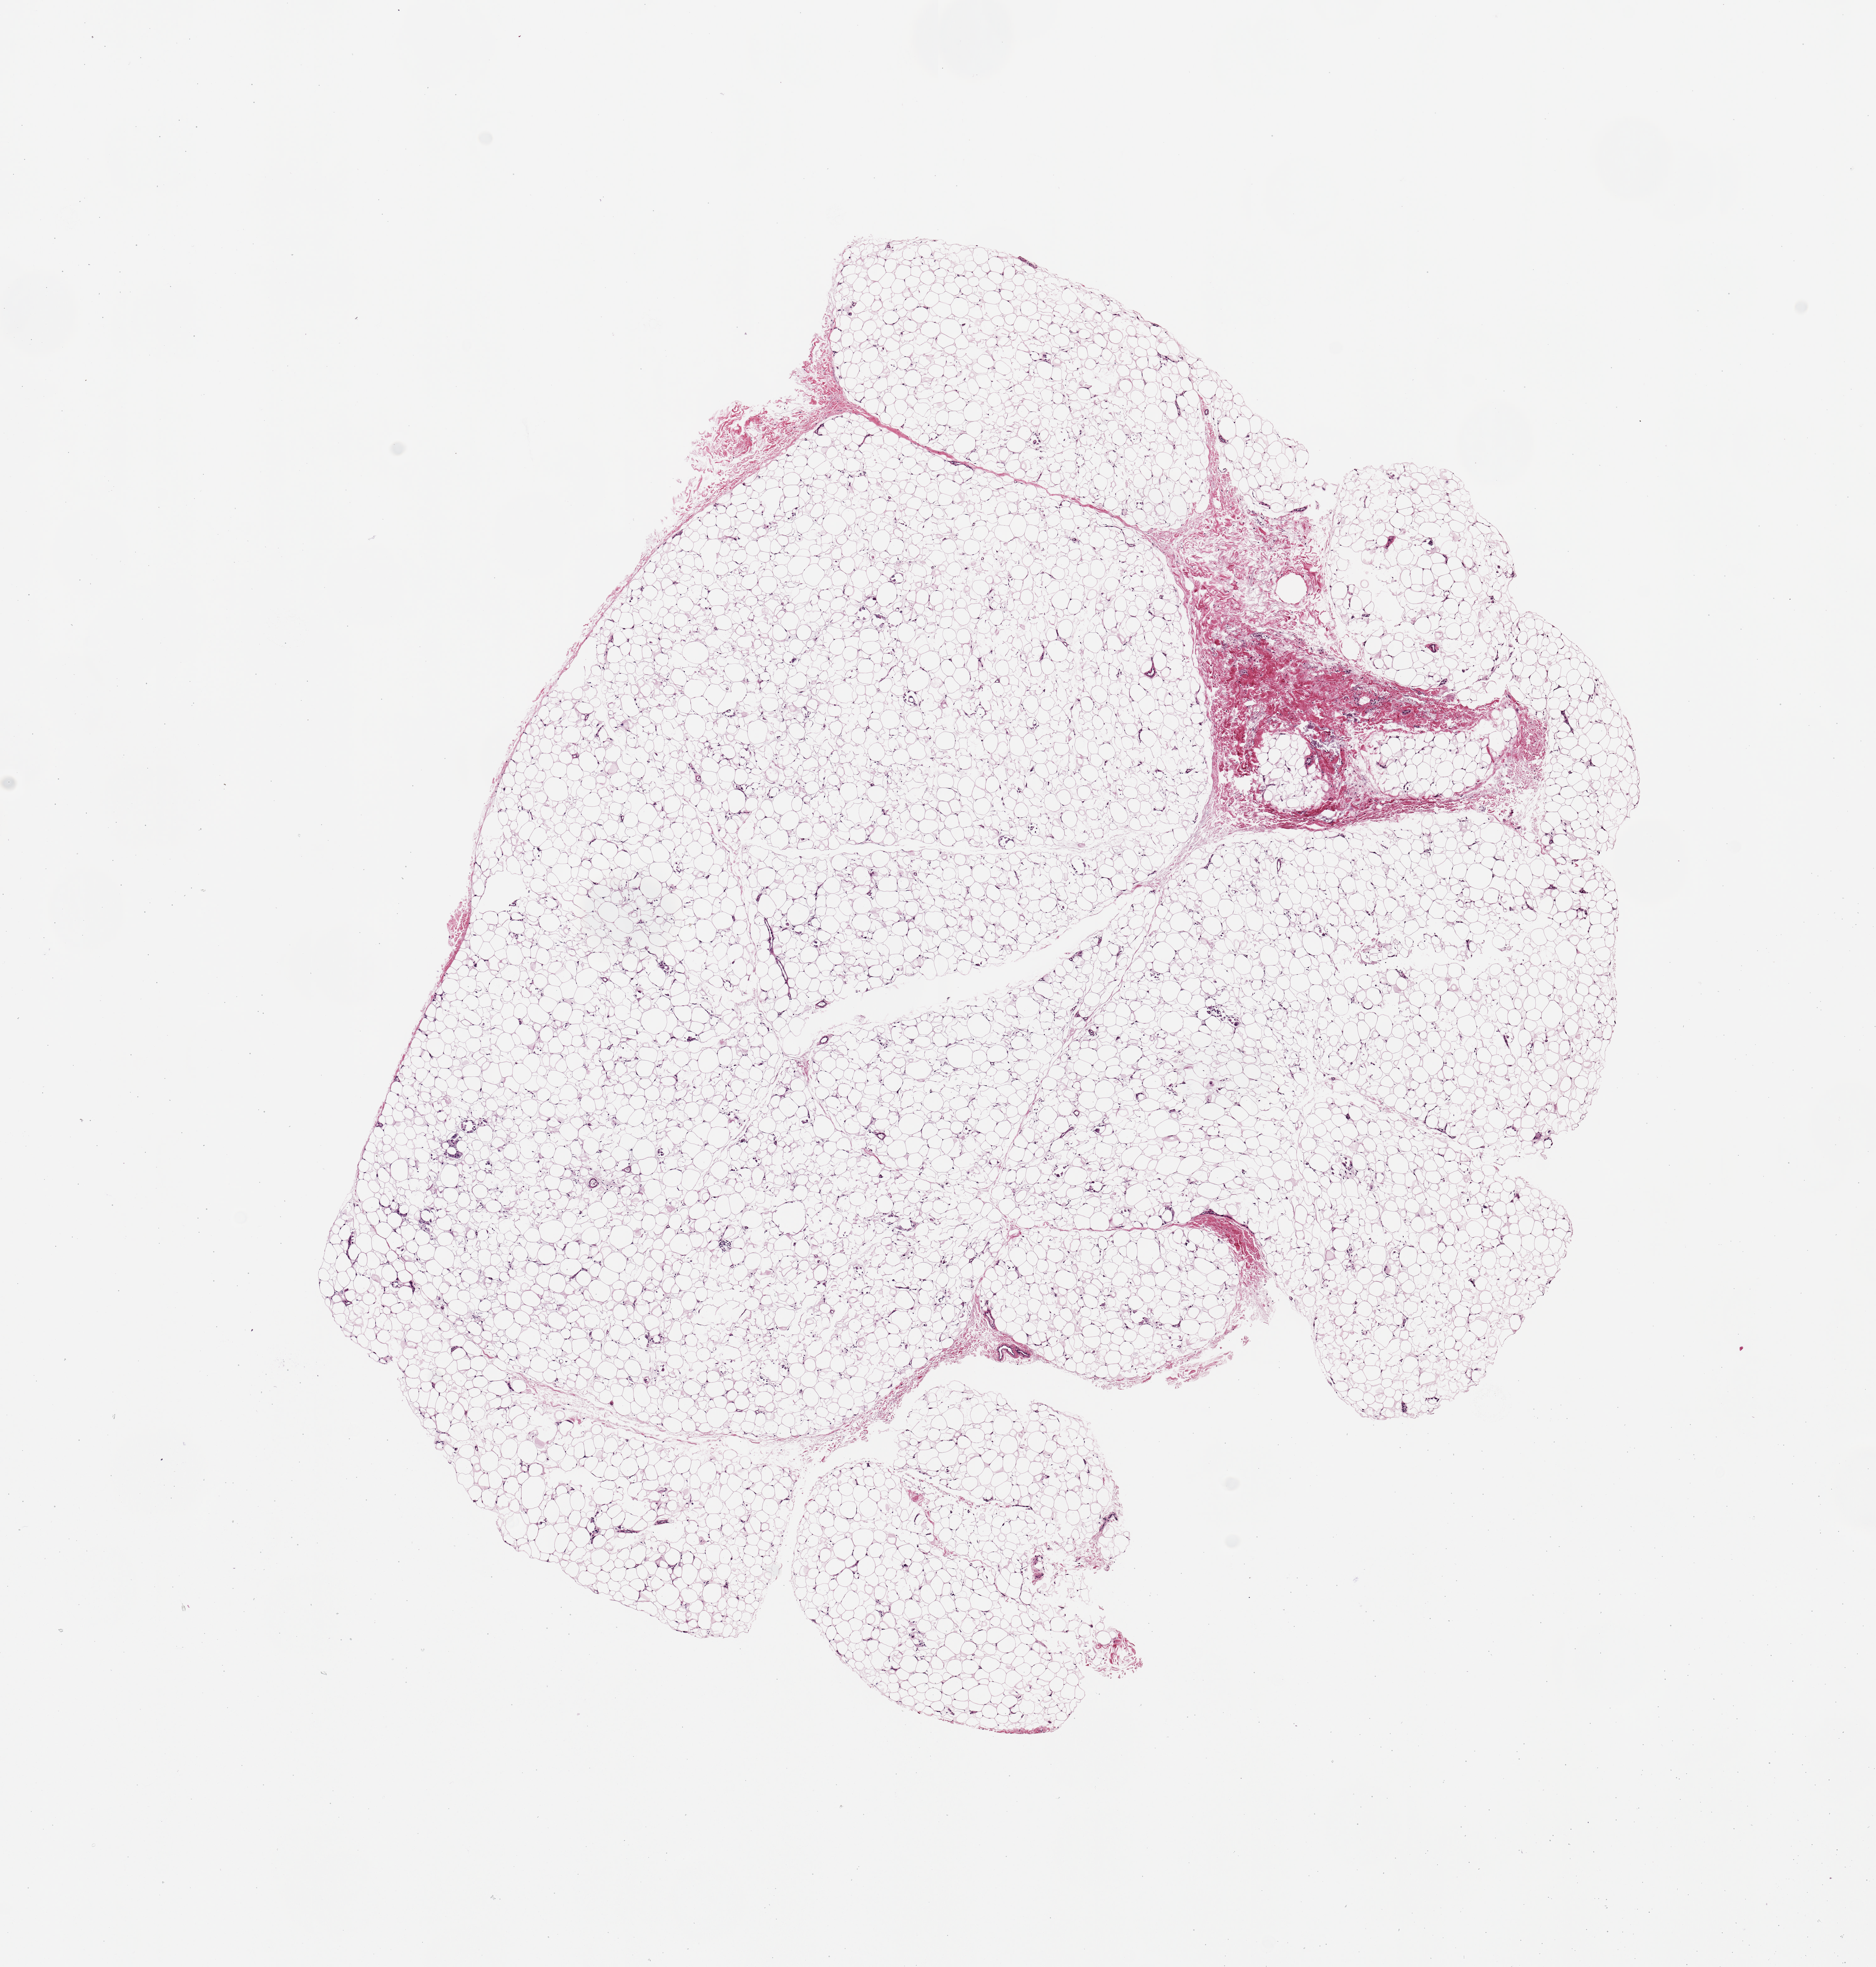
Digitized H&E-stained section, a low-resolution overview of the entire scanned area, about 11.8 x 12.4 mm (slide scanned at 20x), PAXgene-fixed paraffin-embedded (PFPE) section, sampled site (target tissue): adipose tissue, tissue donor sample.
- pathologist's review note for this sample: Well-fixed. 8.5x7mm